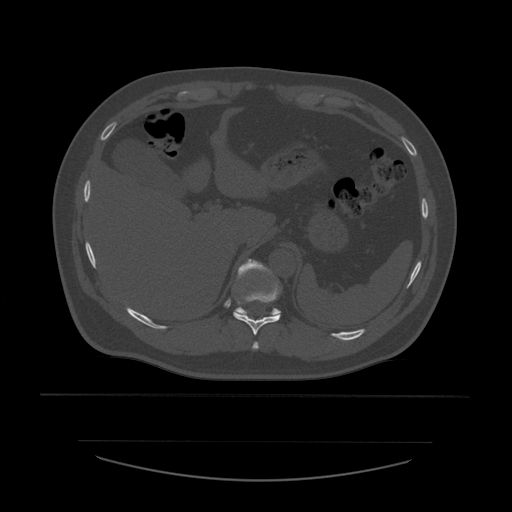
CT including the spine, one axial slice. Position 290 of 532 along the scan axis. Reconstruction kernel STANDARD. 120 kVp. Bone window (W 1800 / L 400 HU). 1.25 mm slice thickness. 512 × 512 image matrix, field of view 441 × 441 mm. Patient age 44 years. From the clinical record (not read from this slice): primary cancer: soft tissue sarcoma.
Structures marked on this image (semi-automatic segmentation, software-assisted and operator-edited):
- T10 vertebra: box from (x=234, y=282) to (x=281, y=336) px
- T11 vertebra: (x=233, y=259)–(x=281, y=315)
- T9 vertebra: (x=252, y=342)–(x=260, y=350)